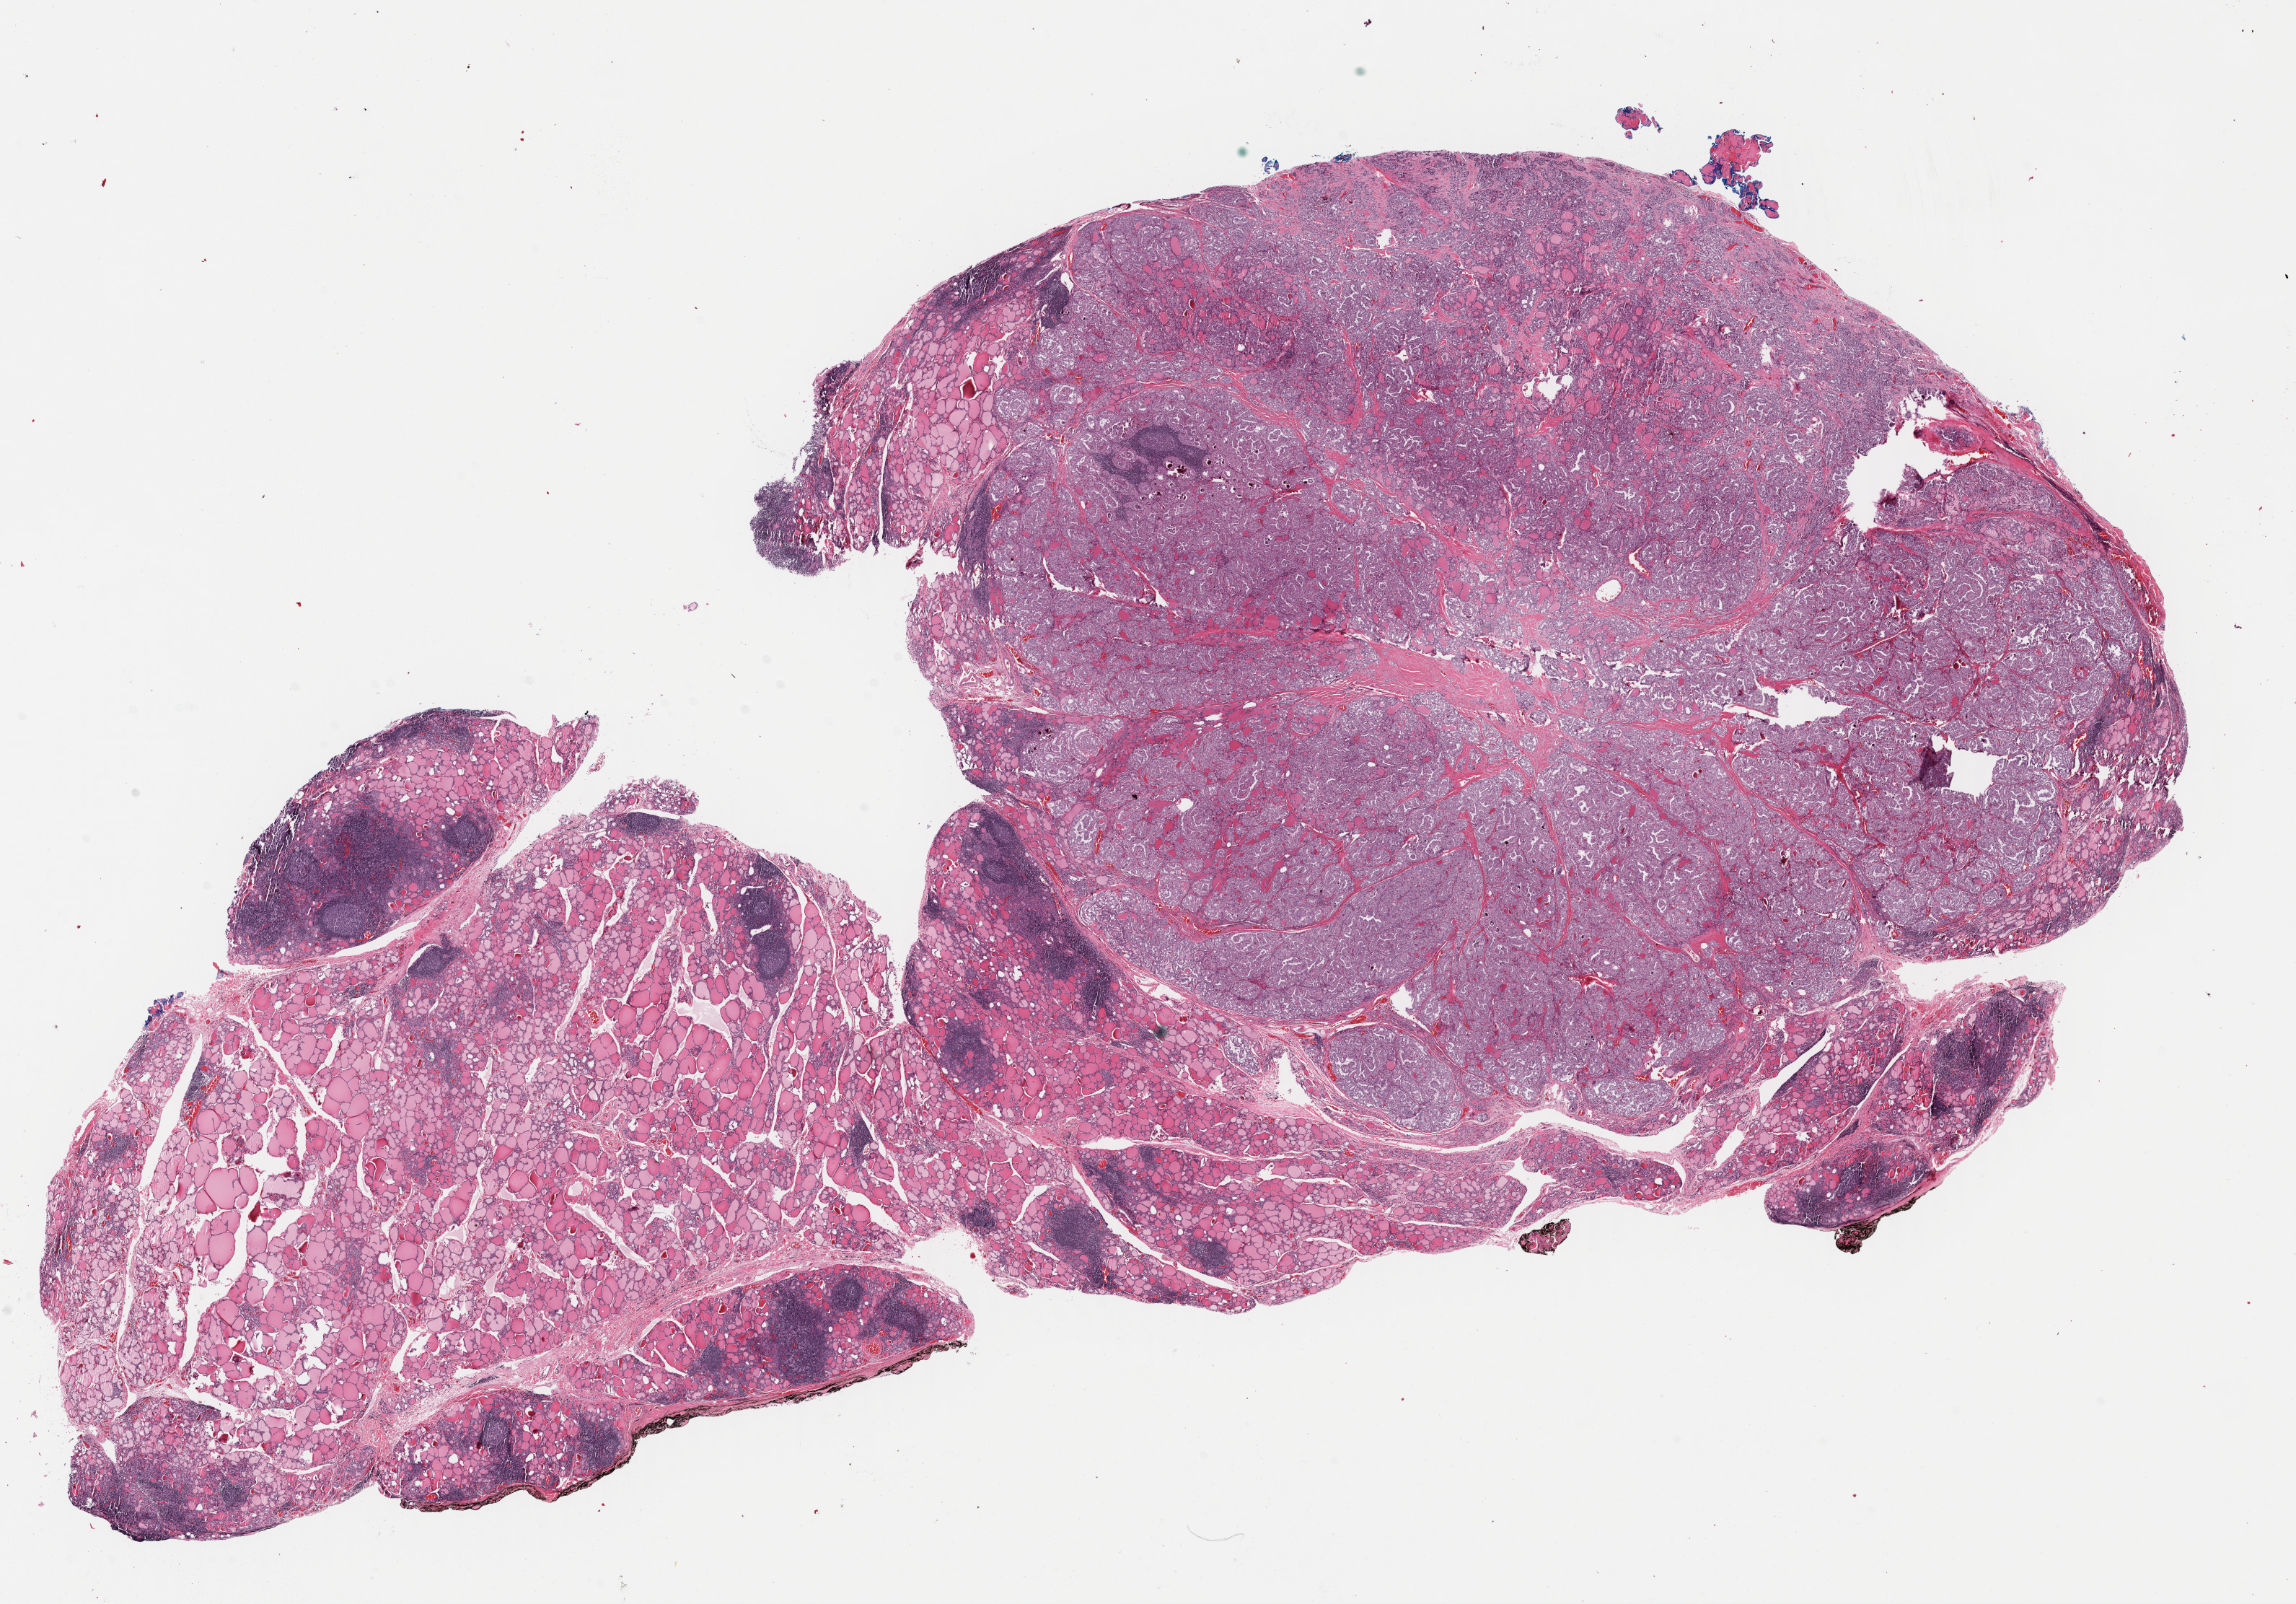
Whole-slide histology image, H&E — a low-resolution overview of the entire scanned area, about 25.0 x 17.5 mm (from a 40x scan), FFPE section, sample: primary tumour, thyroid. Female, age 15 years at initial diagnosis.
Pathologic diagnosis: Papillary adenocarcinoma, NOS (thyroid gland).